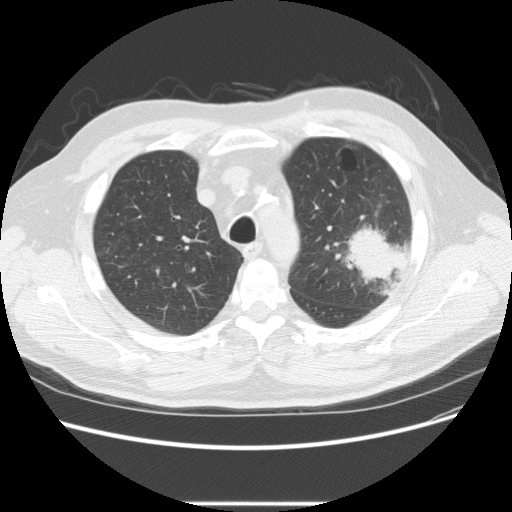
Low-dose screening chest CT, one axial slice. Slice 176 of 233 in the series (ordered by position). Reconstruction kernel STANDARD. Lung window (W 1500 / L -600 HU). 2.5 mm slice thickness. 512 × 512 image matrix, field of view 380 × 380 mm.
Structures marked on this image (outlined manually by an expert reader):
- lesion 1 (tumor, upper lobe of left lung): bounding box [x1, y1, x2, y2] px = [345, 226, 401, 287]